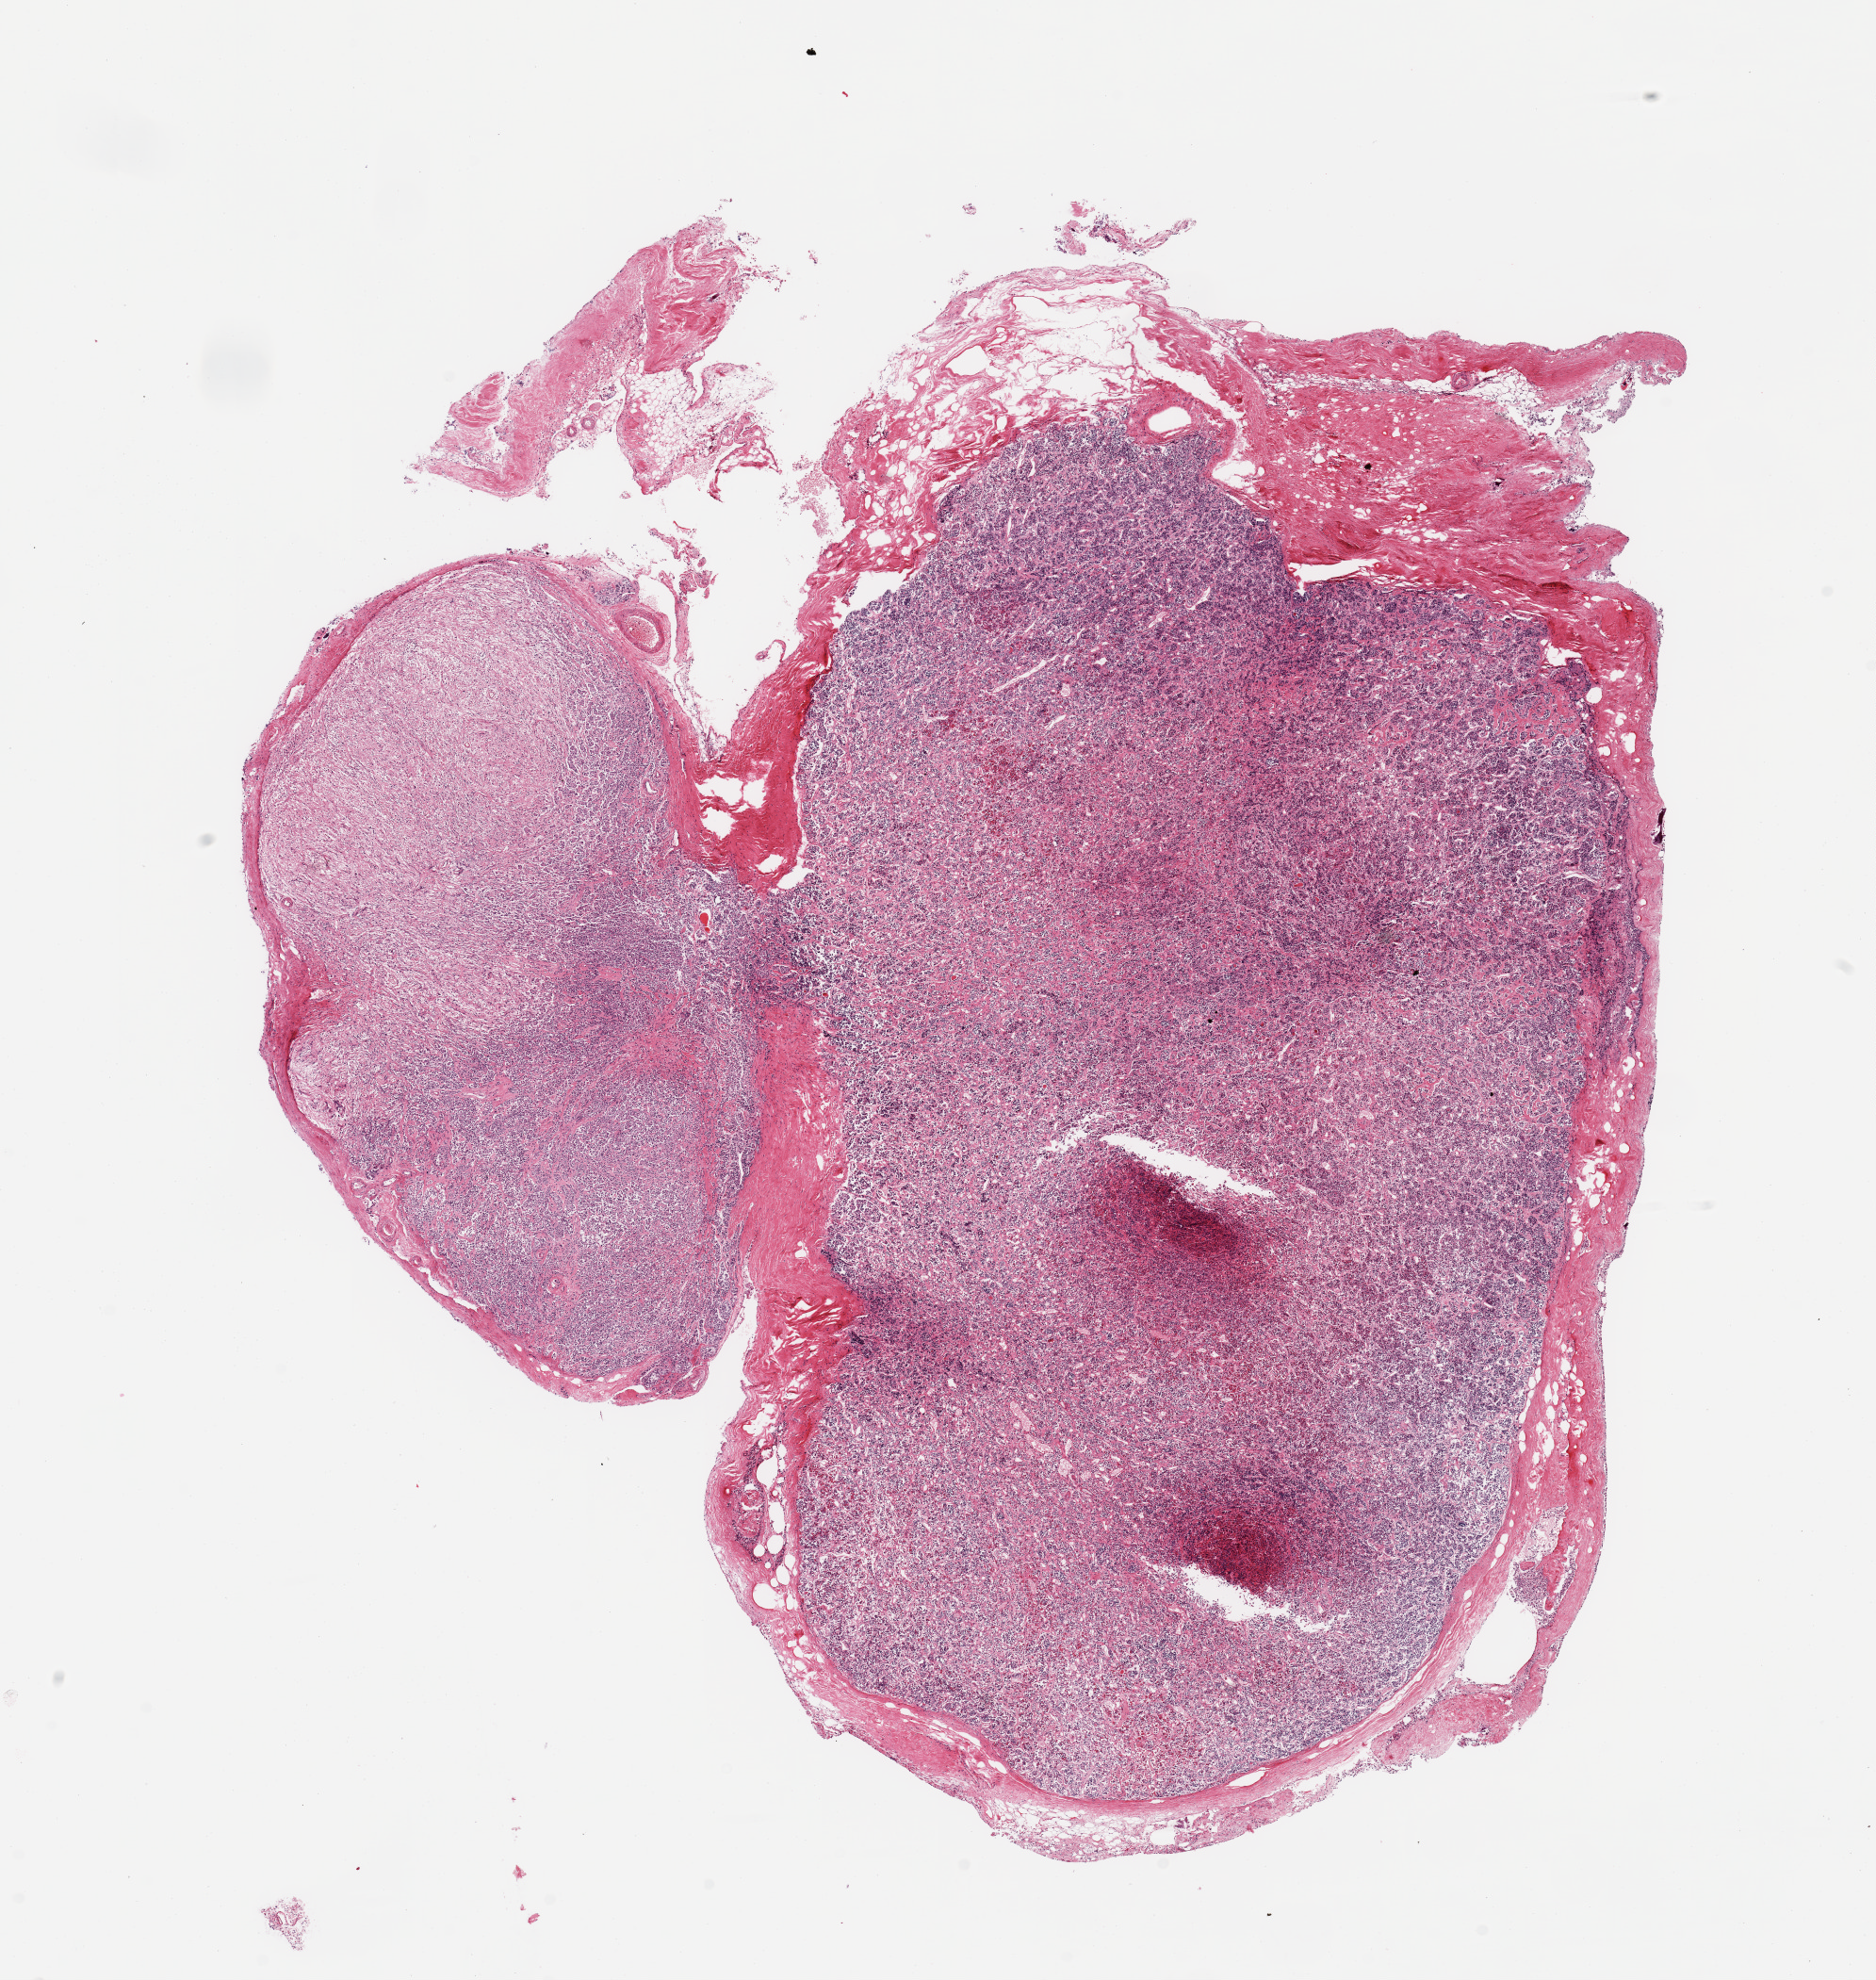
Digitized H&E-stained section — low-resolution overview of the scanned area, about 15.8 x 16.6 mm (from a 20x scan), PAXgene-fixed paraffin-embedded (PFPE) section, section of pituitary (target tissue), donor tissue sample. Male donor.
Pathologist's review note for this sample: 1 piece; adenohypophysis, neurohypophysis.